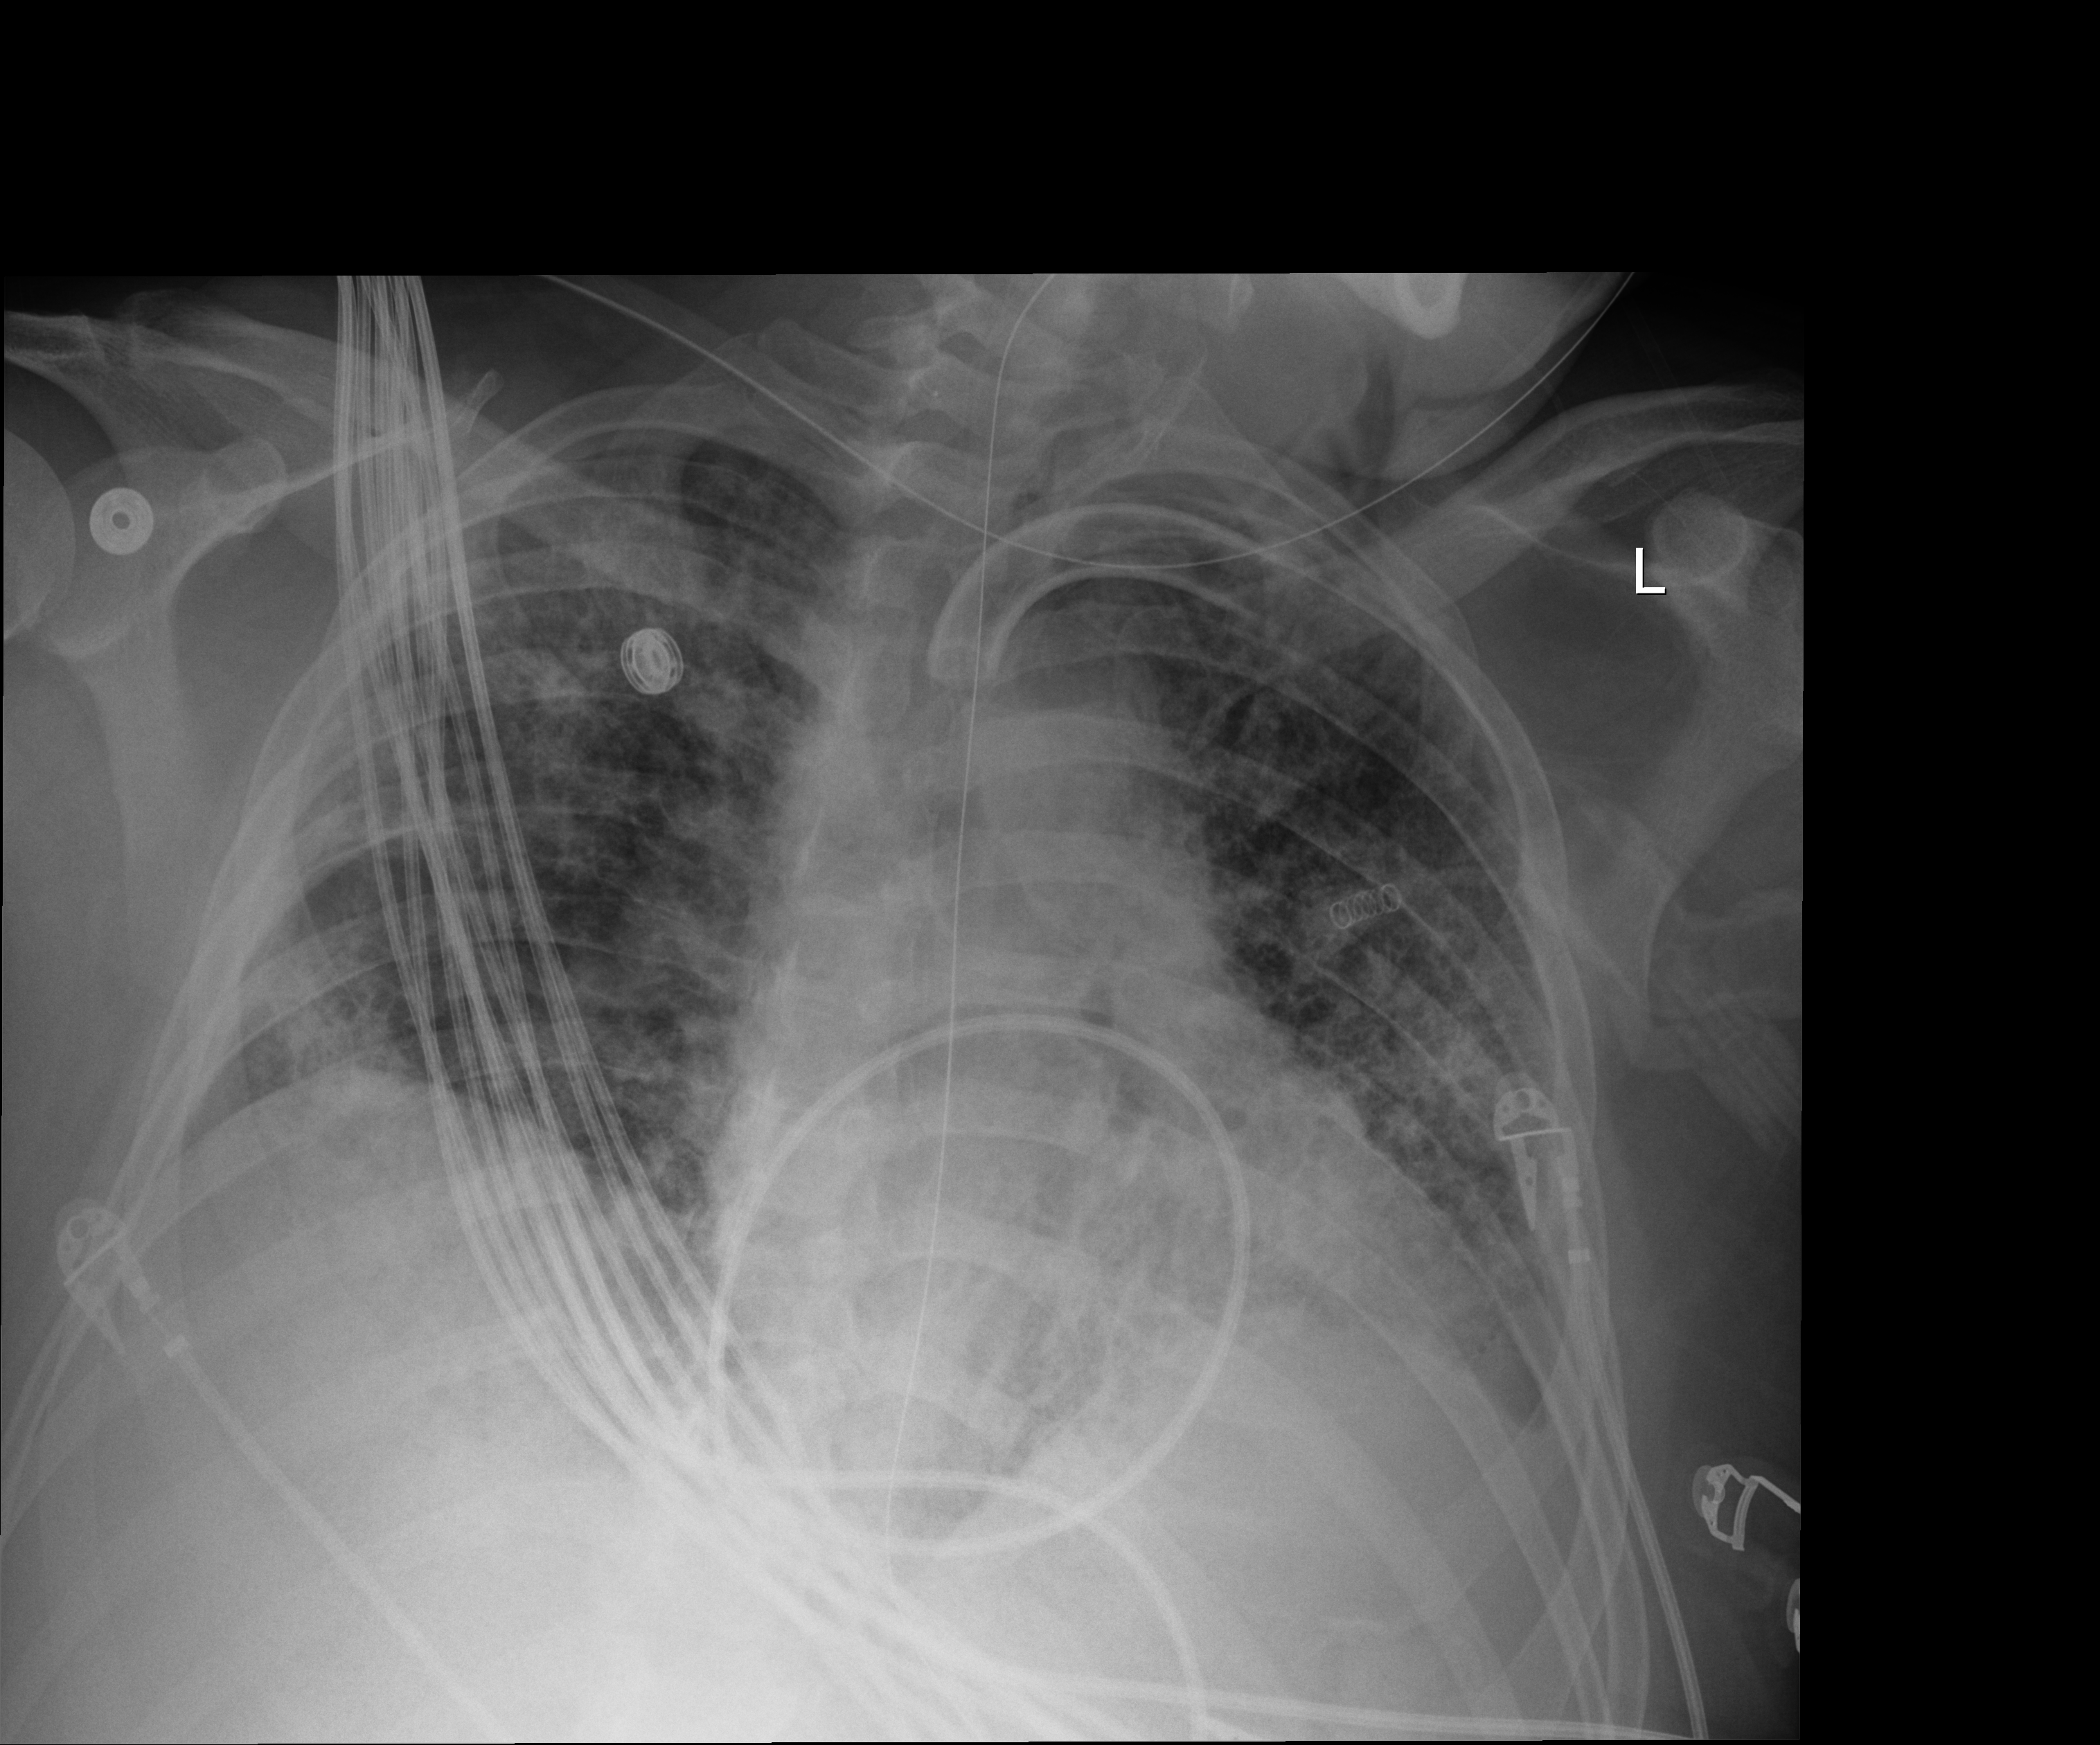
Bedside chest radiograph (digital radiography); anteroposterior (AP) projection. Male patient hospitalised with COVID-19, age 18–59 years.
Hospital-stay facts (about this admission, not read from this image; timing relative to this image not recorded): smoking status (admission record): never.